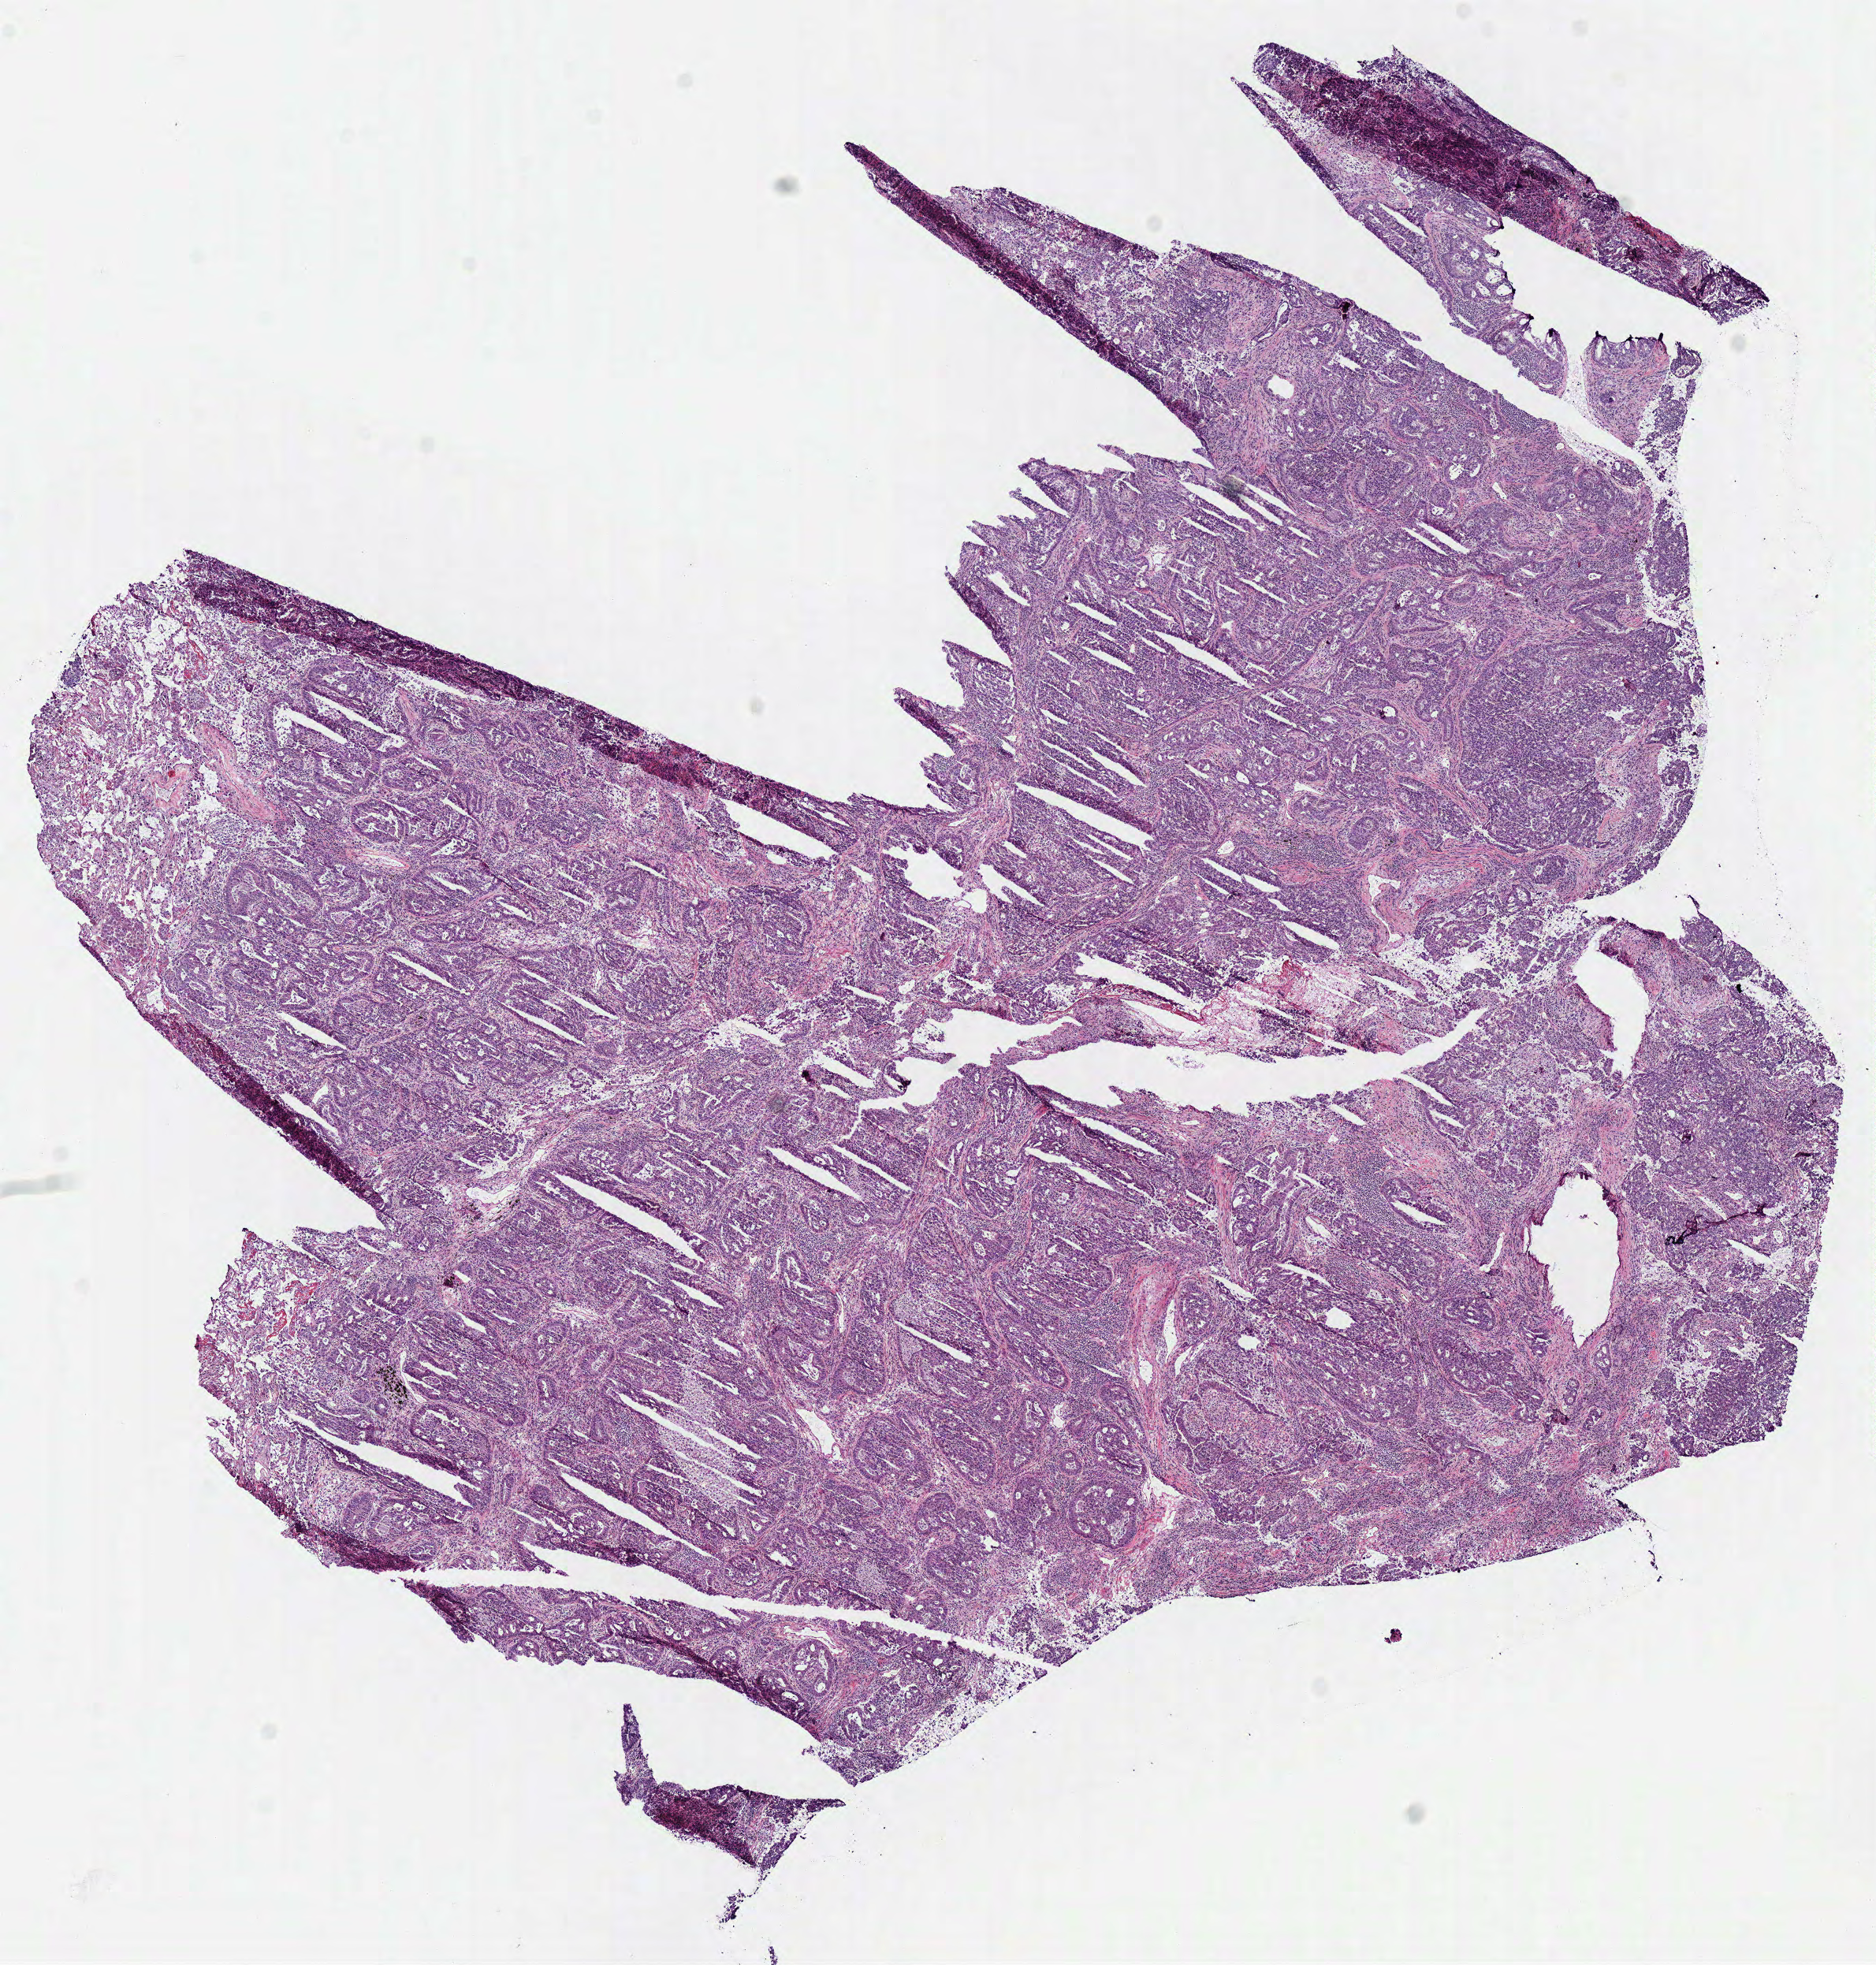
Digitized H&E tissue section (whole slide) — whole scanned area (about 9.4 x 9.8 mm, acquisition: 40x scan) shown as a low-resolution overview; frozen section; sample: primary tumour, lung. Male patient; age at initial diagnosis 70 years. Slide review estimates, as recorded: tumour cells 82%, tumour nuclei 65%, normal cells 8%, stromal cells 10%, necrosis 0%.
Histologic diagnosis: Adenocarcinoma, NOS. TNM: T1a N0 M0. AJCC pathologic stage: IA.